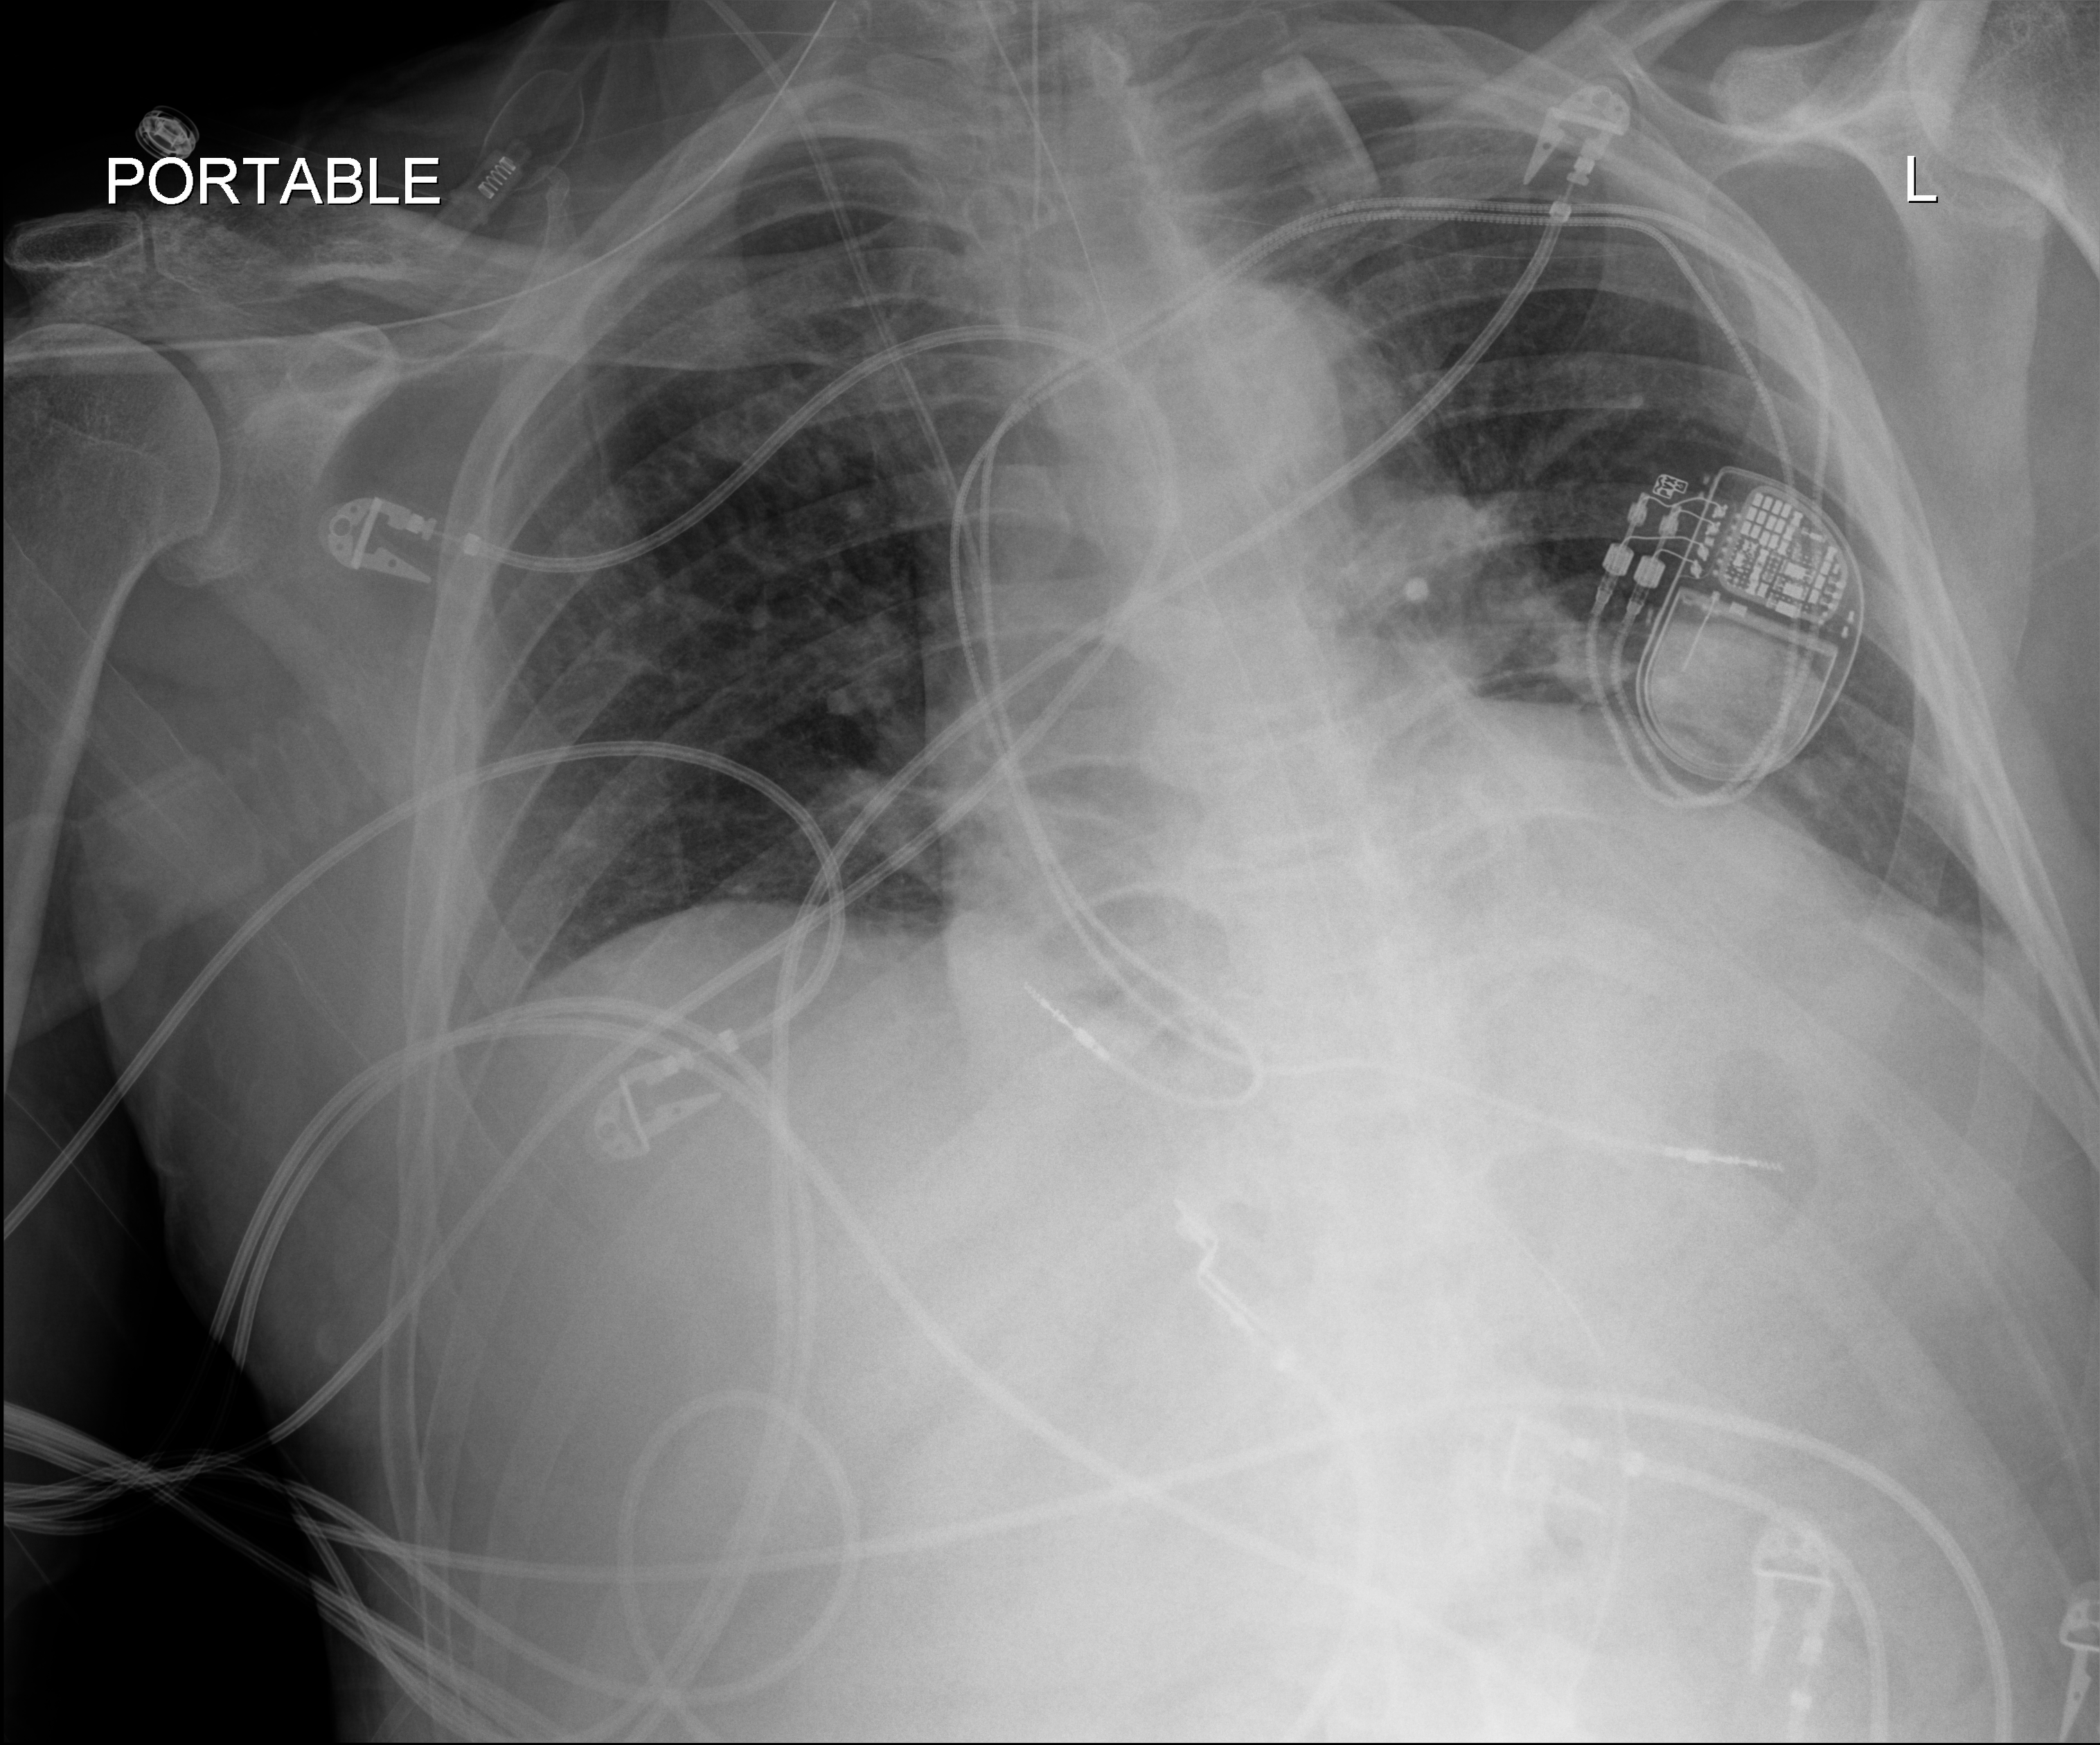
Chest X-ray (portable), anteroposterior (AP) projection. Patient hospitalised with COVID-19; male, aged 60–74 years.
Admission-level facts for this patient (not findings on this image; timing relative to this image not recorded): mechanically ventilated during this hospital stay: yes; length of hospital stay: 41 days; admitted to intensive care during this hospital stay: yes.